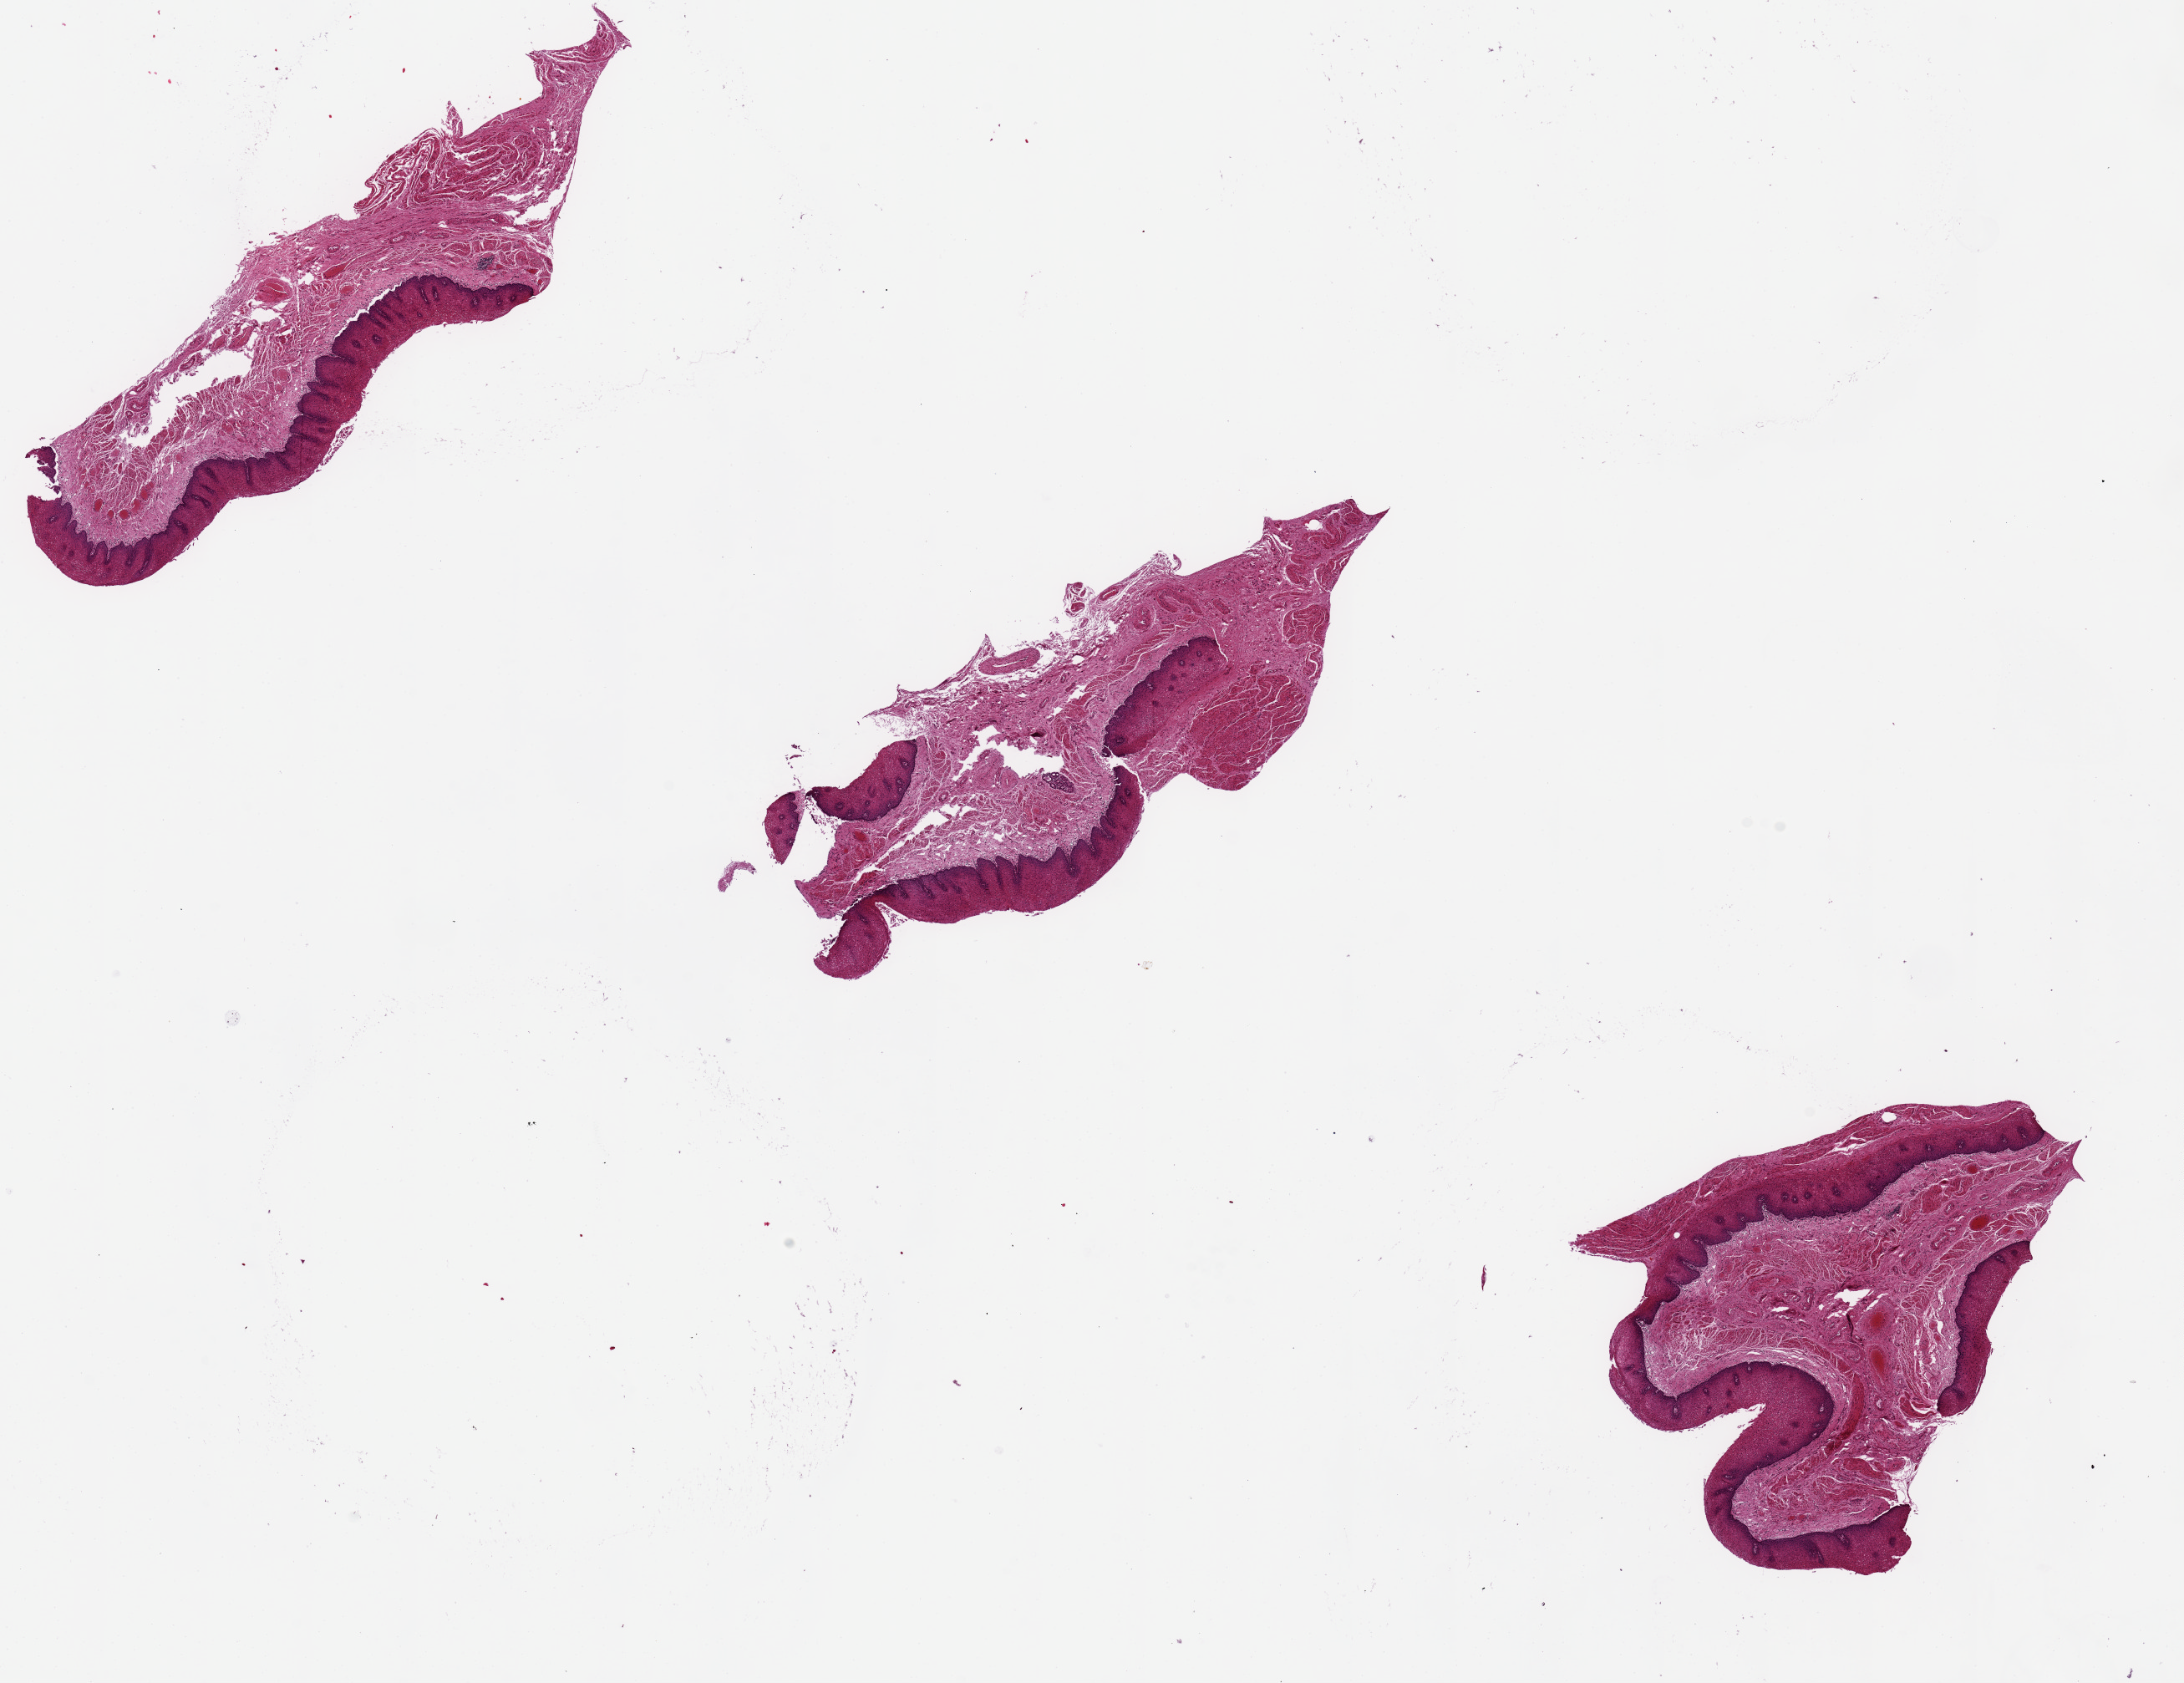
Haematoxylin and eosin whole-slide image, brightfield — low-resolution overview of the scanned area, about 20.7 x 15.9 mm (acquisition: 20x scan), PAXgene-fixed paraffin-embedded (PFPE) section, section of esophageal mucous membrane (target tissue), donor tissue sample. Donor: female.
Pathologist's review note for this sample: 3 pieces.